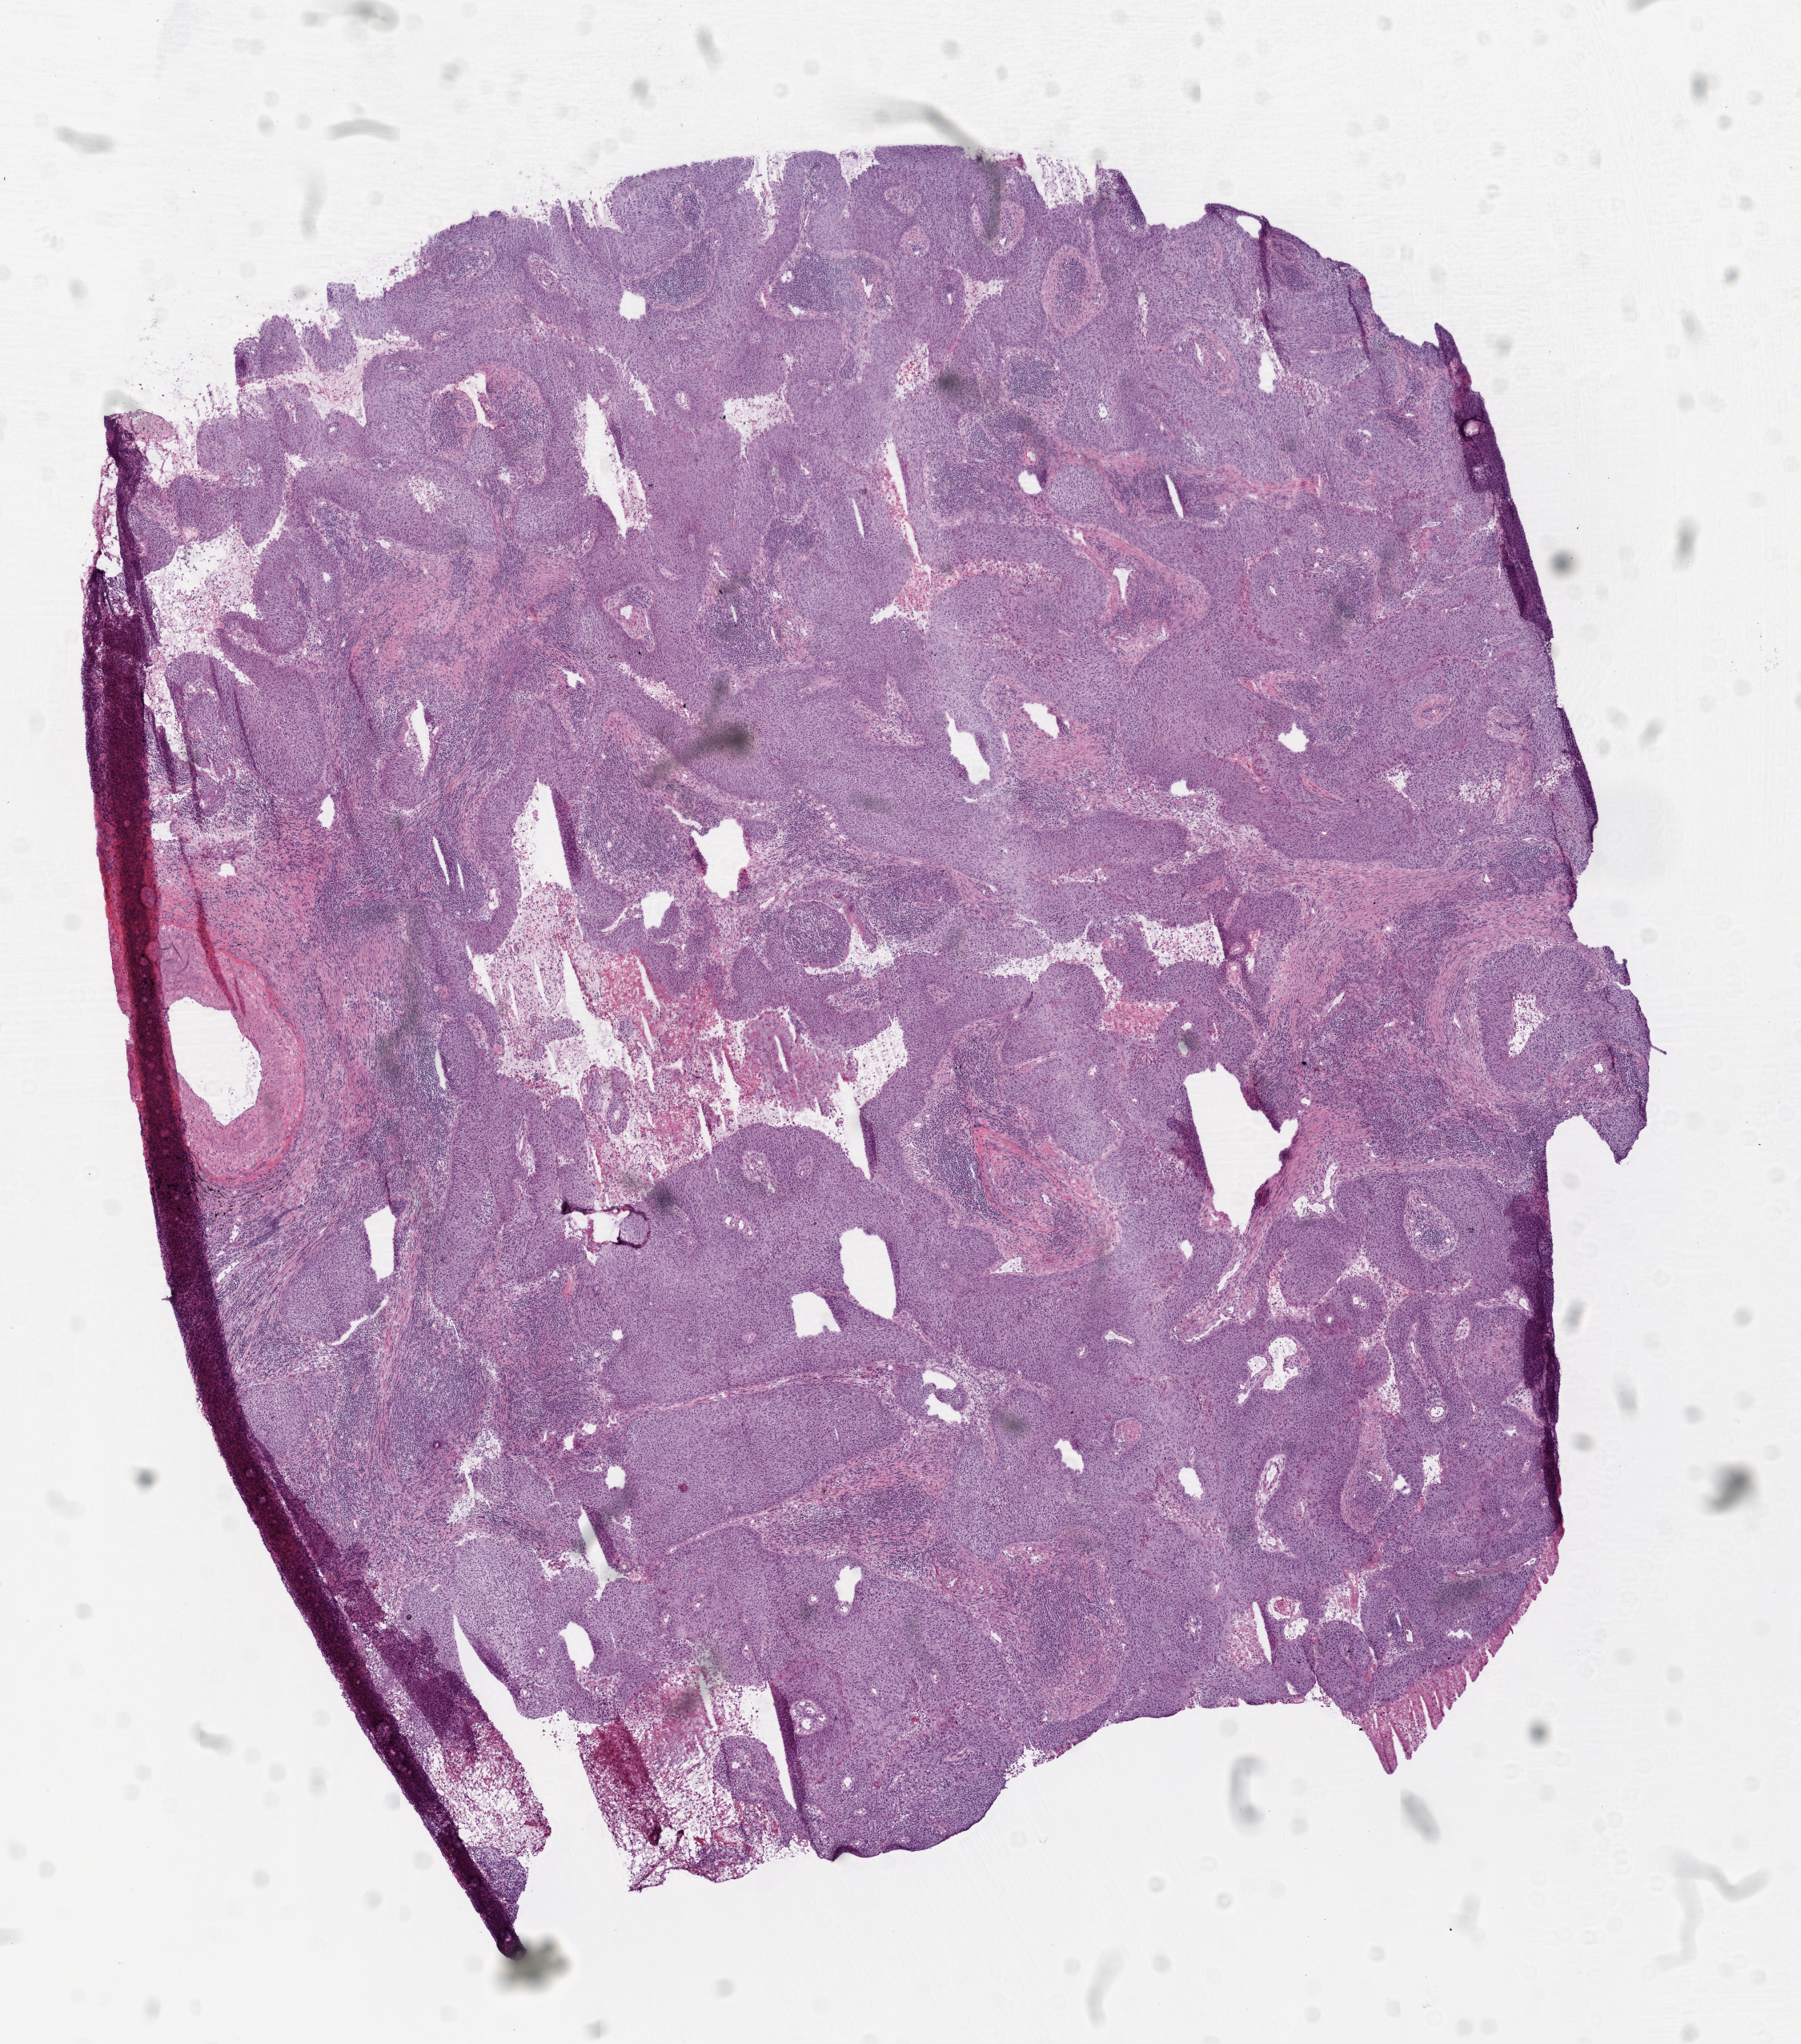
Digitized Hematoxylin and eosin (H&E) stained tissue section (whole slide), whole scanned area (about 9.0 x 10.2 mm) shown as a low-resolution overview. Frozen section from the top of the tissue portion. Sample: primary tumour, lung. Patient: male, age at initial diagnosis 67 years. Pathologist review of this section (percent, as recorded): tumour cells 80%, tumour nuclei 60%, normal cells 0%, stromal cells 10%, necrosis 10%. Inflammatory infiltration, as recorded: lymphocyte infiltration 30%, monocyte infiltration 0%, neutrophil infiltration 0%.
* histologic diagnosis: Squamous cell carcinoma, NOS (lower lobe, lung)
* TNM: T2 N3 M0
* AJCC pathologic stage: IIIB (6th edition)